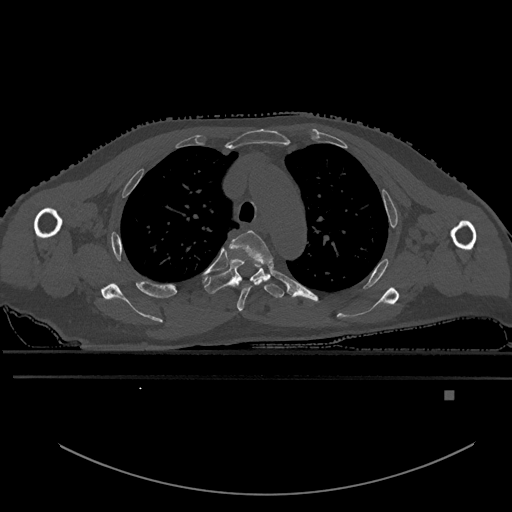
CT including the spine, one axial slice; position 425 of 969 along the scan axis; bone window (W 1800 / L 400 HU); 0.5 mm slice thickness; 512 × 512 image matrix, field of view 456 × 456 mm. Male patient, age 82 years. From the clinical record (not read from this slice): primary cancer: prostate.
Structures marked on this image (semi-automatically segmented with operator editing):
- T3 vertebra: bounding box [x1, y1, x2, y2] px = [230, 230, 273, 312]
- T4 vertebra: [203, 259, 285, 298]